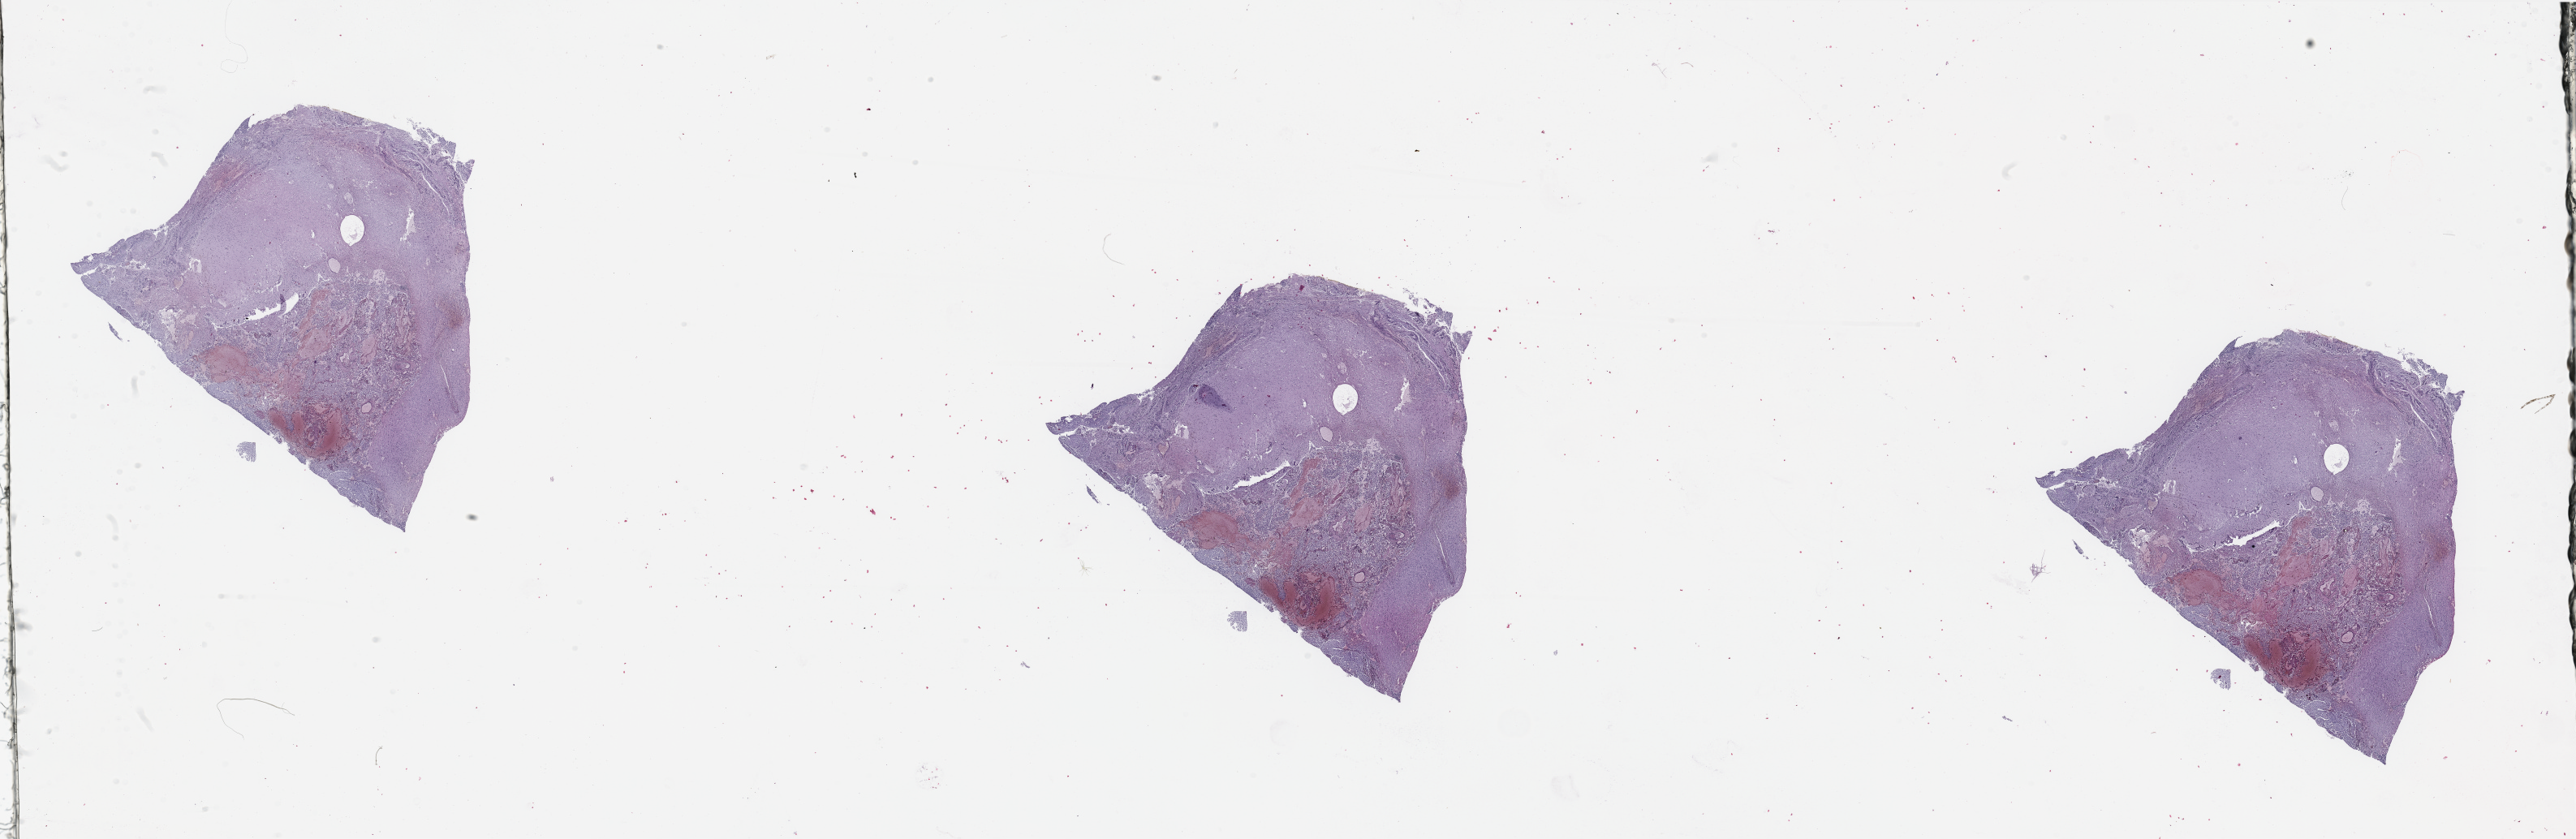
Whole-slide histology image, H&E, a low-resolution overview of the entire scanned area, about 50.2 x 16.4 mm (slide scanned at 20x). Tumour tissue sample, brain. 40-year-old male patient.
• diagnosis: Glioblastoma
• primary tumour site (as recorded): parietal lobe